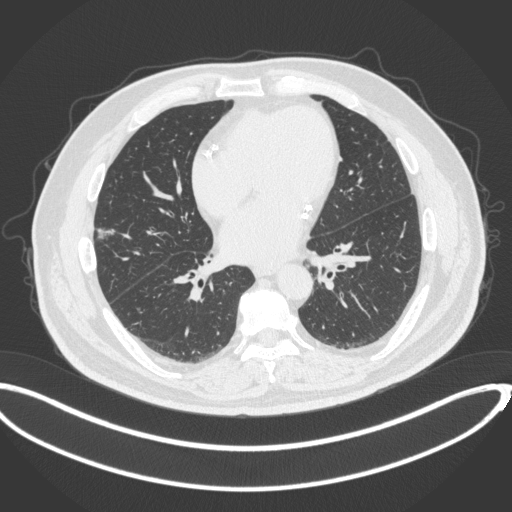
Chest CT, one axial slice; position 142 of 342 along the scan axis; reconstruction kernel B31f; 120 kVp; lung window (W 1500 / L -600 HU); 512 × 512 image matrix, field of view 427 × 427 mm. Male patient, age 68 years. From the clinical record (not read from this slice): clinical TNM (as recorded): T1c N0 M0; histopathological grade: G2.
Annotated regions visible in this slice (bounding box drawn by a radiologist):
- lung tumour (recorded histology: adenocarcinoma): box from (x=95, y=226) to (x=119, y=240) px